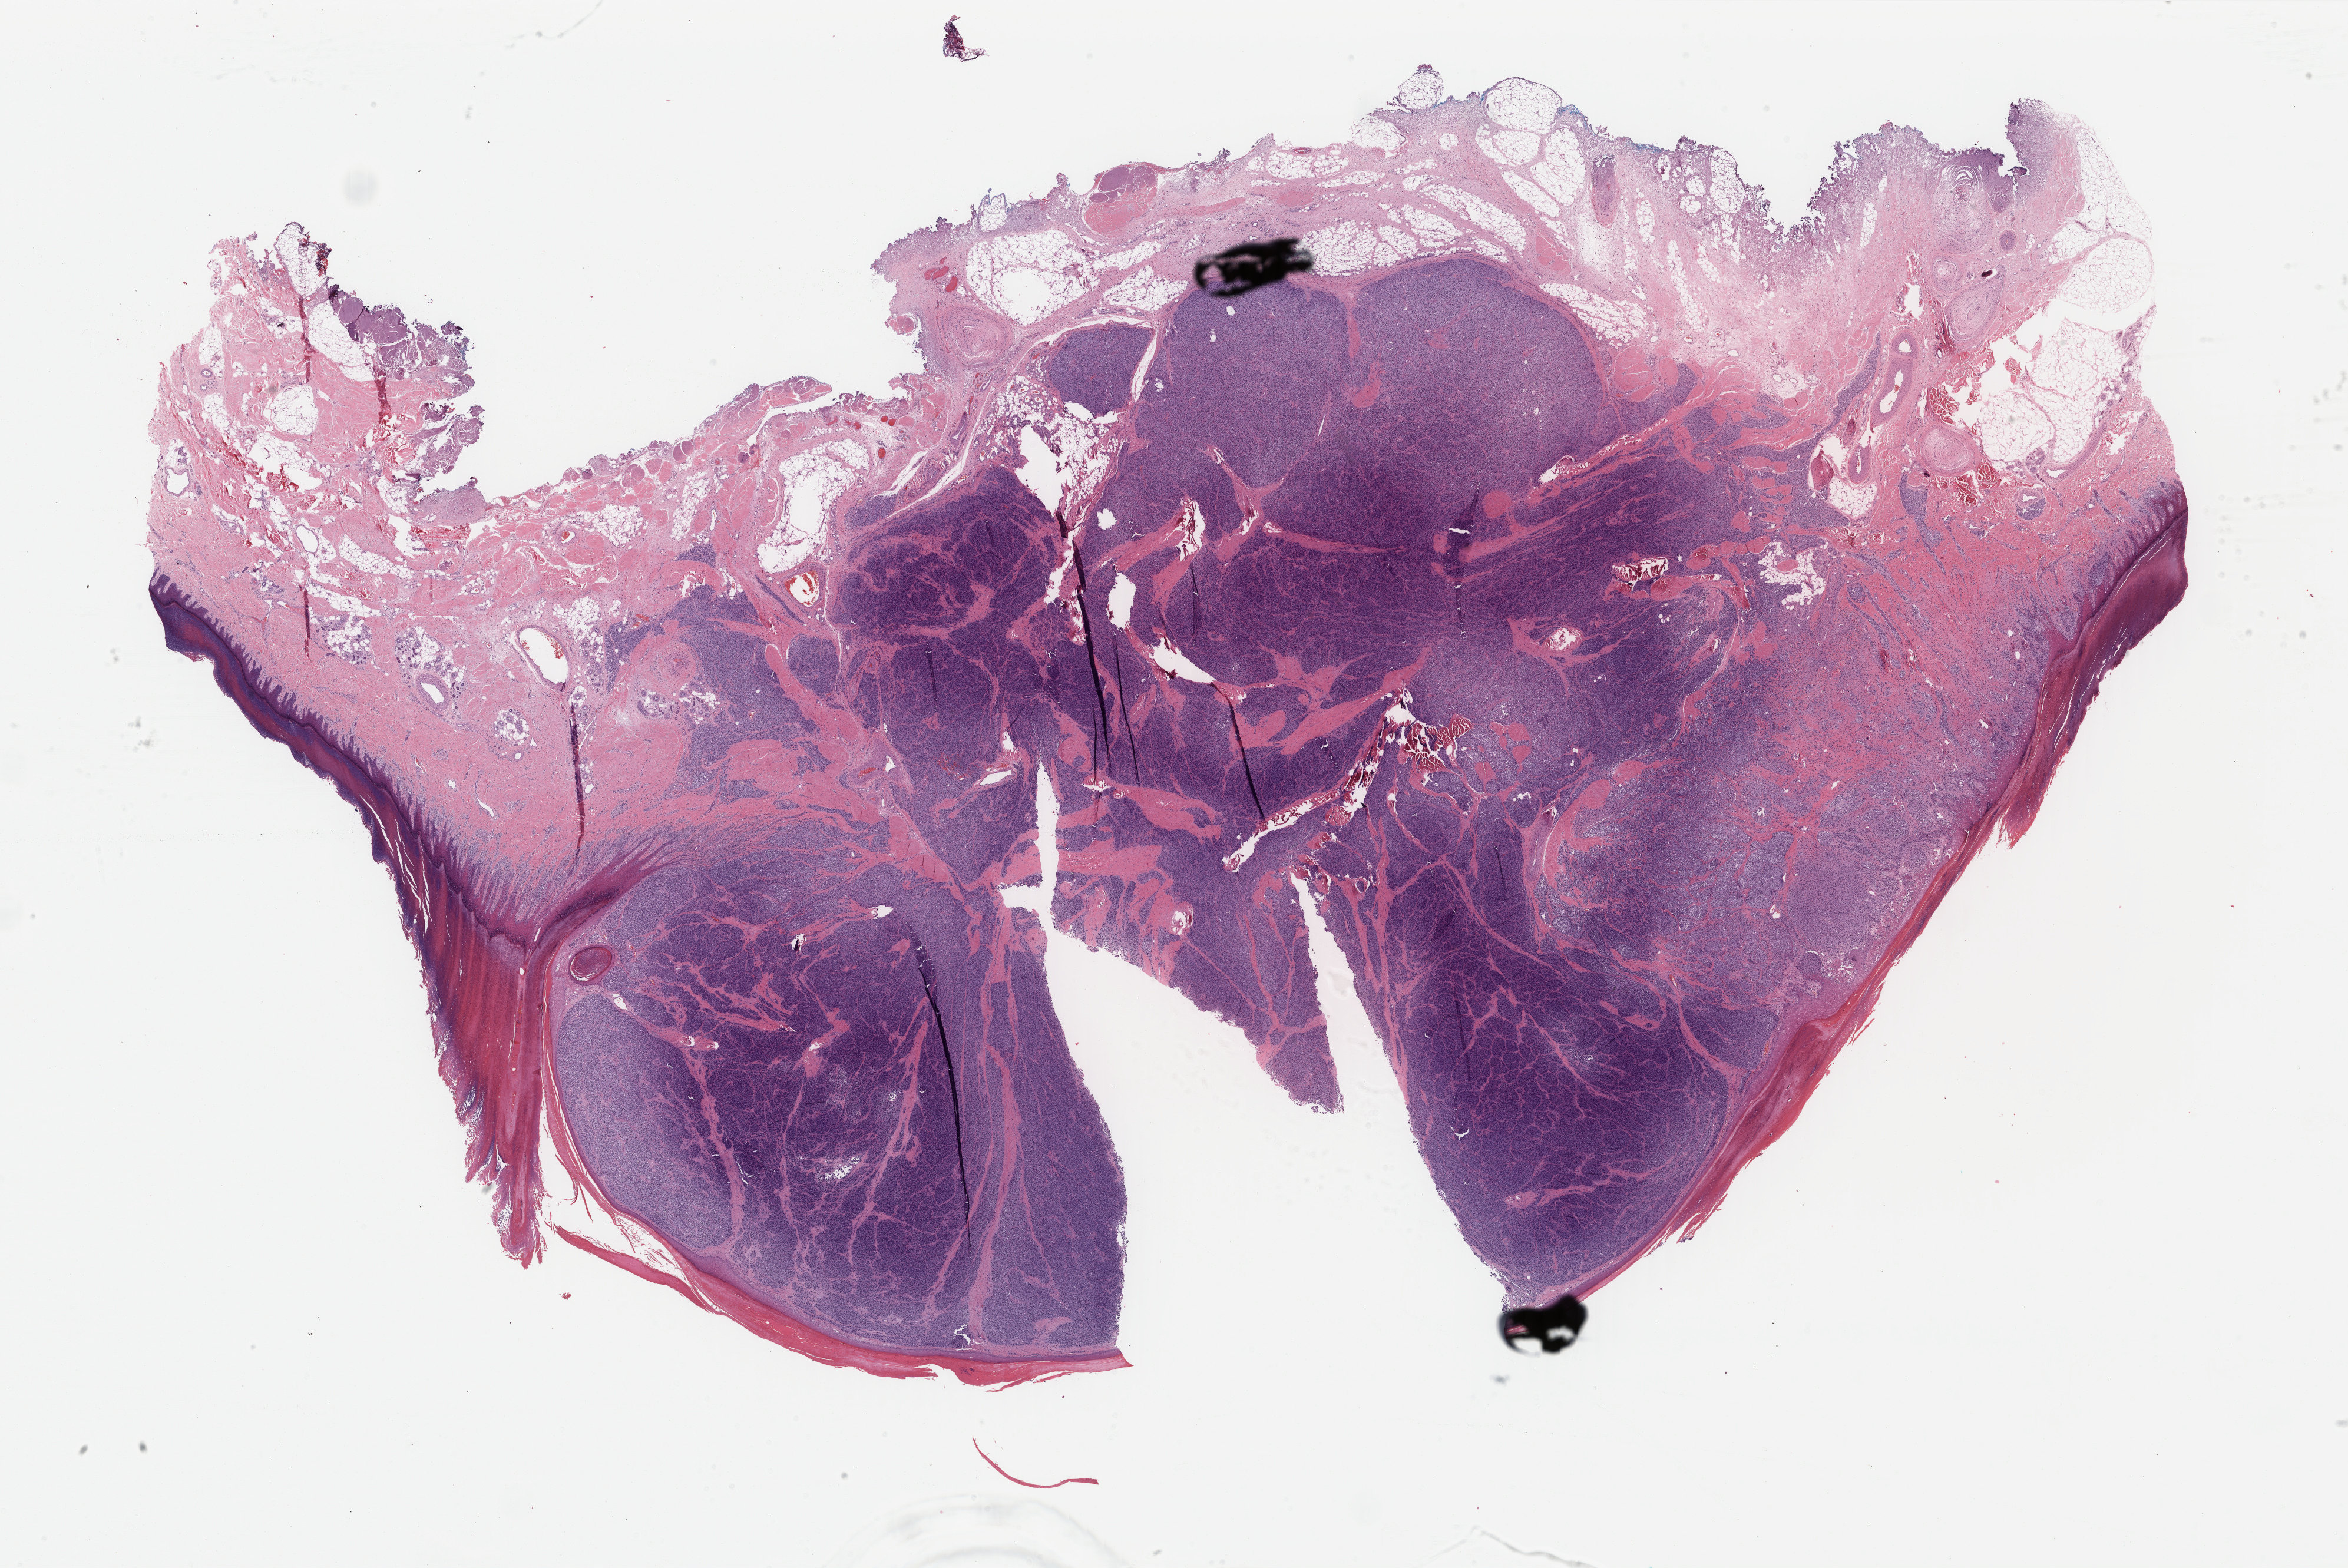
Whole-slide histology image, Hematoxylin and eosin (H&E) stained — shown as a low-resolution overview of the whole scanned area (about 31.6 x 21.1 mm, slide scanned at 40x). Formalin-fixed paraffin-embedded (FFPE) diagnostic section. Skin, primary tumour sample. Male patient; age at initial diagnosis 51 years.
Pathologic diagnosis: Acral lentiginous melanoma, malignant.